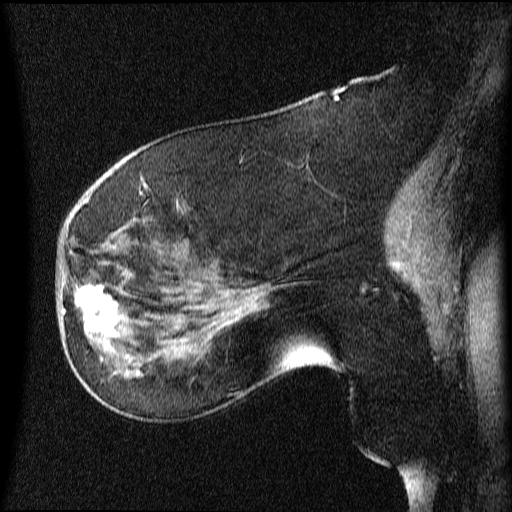
Breast MRI (dynamic contrast-enhanced), one sagittal slice. Slice 28 of 64 in the series (ordered by position). Dynamic contrast-enhanced series, image 2 of 4 at this slice position (ordered by acquisition). 1.5 T. TE 4.2 ms, TR 9 ms. 512 × 512 image matrix, field of view 200 × 200 mm. Female patient, age 63 years.
Annotated regions visible in this slice (semi-automatic segmentation, software-assisted and operator-edited):
- analysis volume of interest (the breast-tissue region the enhancement analysis was run in; not a lesion): box from (x=66, y=272) to (x=131, y=353) px
- tumour enhancement mask (voxels above the 70 % enhancement threshold inside the analysis volume of interest): (x=77, y=286)–(x=117, y=349)